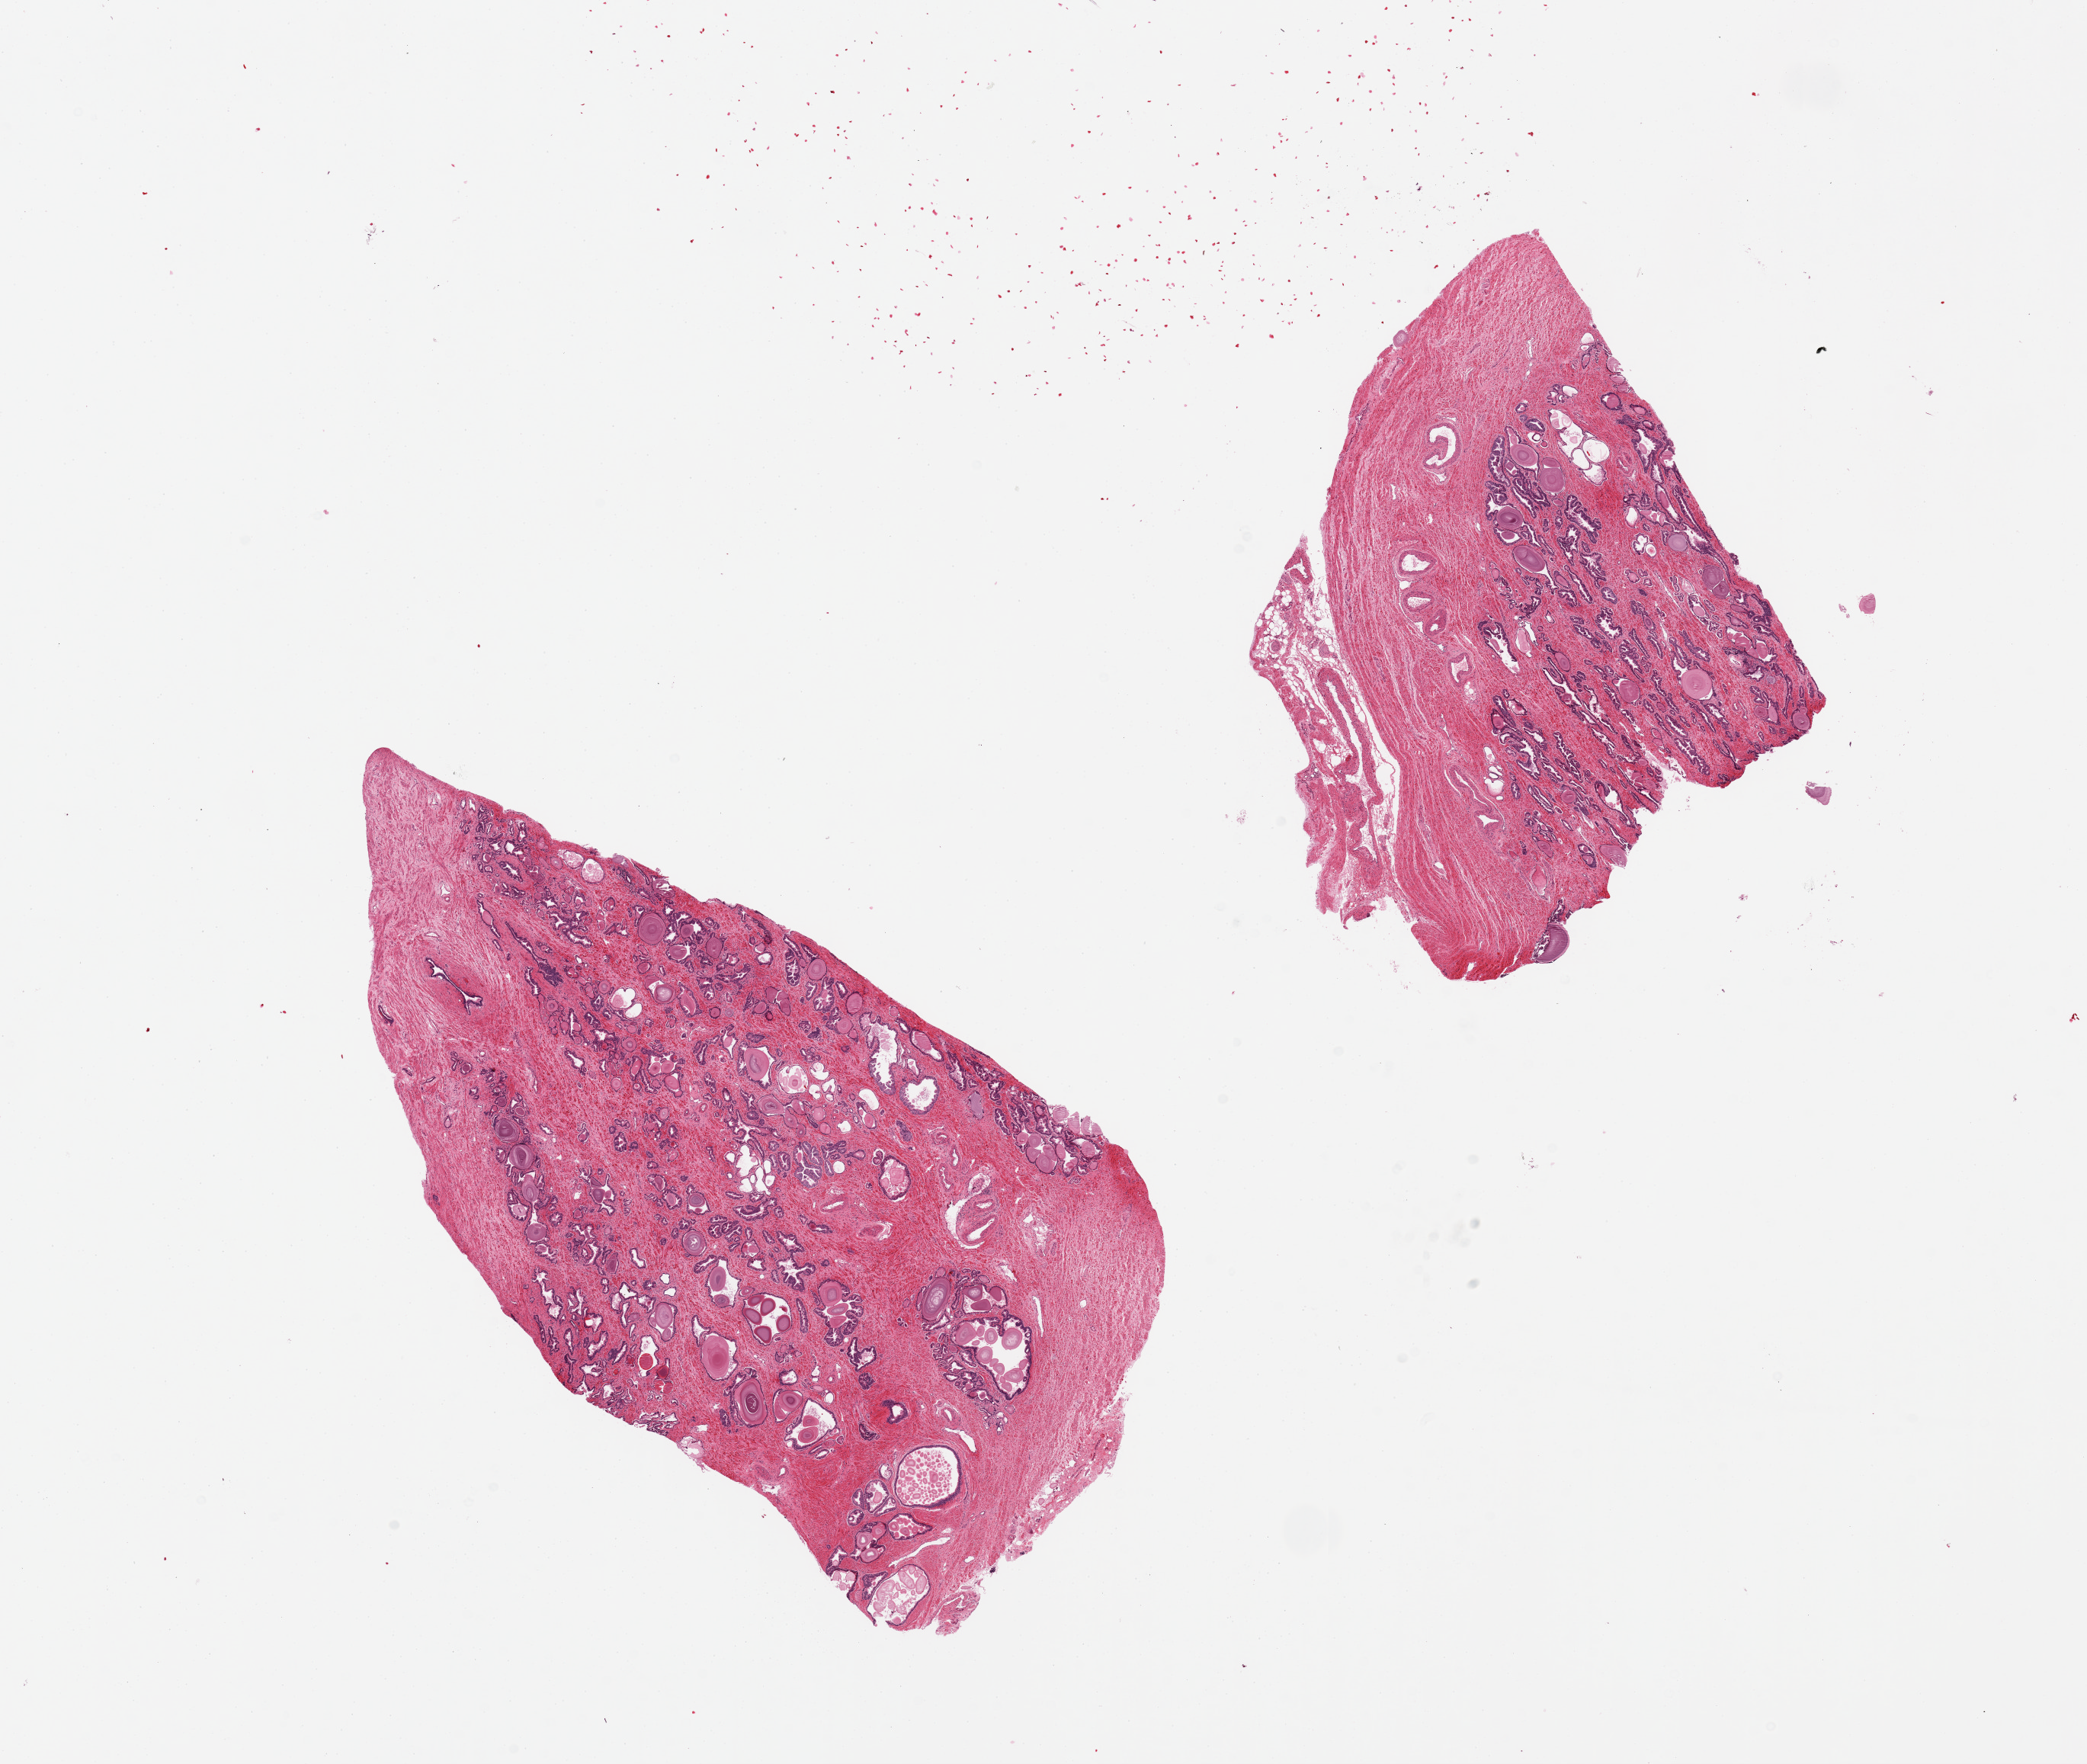
Whole-slide image, H&E stain, a low-resolution overview of the entire scanned area, about 21.7 x 18.3 mm (slide scanned at 20x). PAXgene-fixed, paraffin-embedded tissue. Target tissue: prostate. Tissue donor sample. Donor sex: male.
• review note (as recorded): 2 pieces. 10% peripheral fat on 1